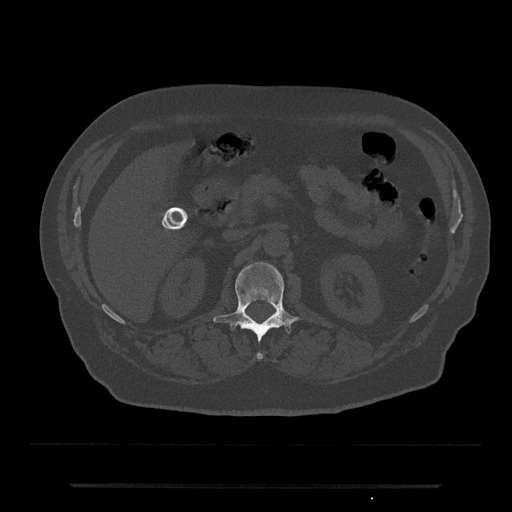
CT including the spine, one axial slice. Slice 535 of 797 in the series (ordered by position). 120 kVp. Bone window (W 1800 / L 400 HU). 0.5 mm slice thickness. 512 × 512 image matrix, field of view 434 × 434 mm. Male patient, age 80 years. From the clinical record (not read from this slice): primary cancer: prostate; vertebrae with lytic lesions (as recorded): L1, T11.
Structures marked on this image (semi-automatic segmentation, software-assisted and operator-edited):
- L1 vertebra: bounding box <213,262,298,360> (left, top, right, bottom; pixels)